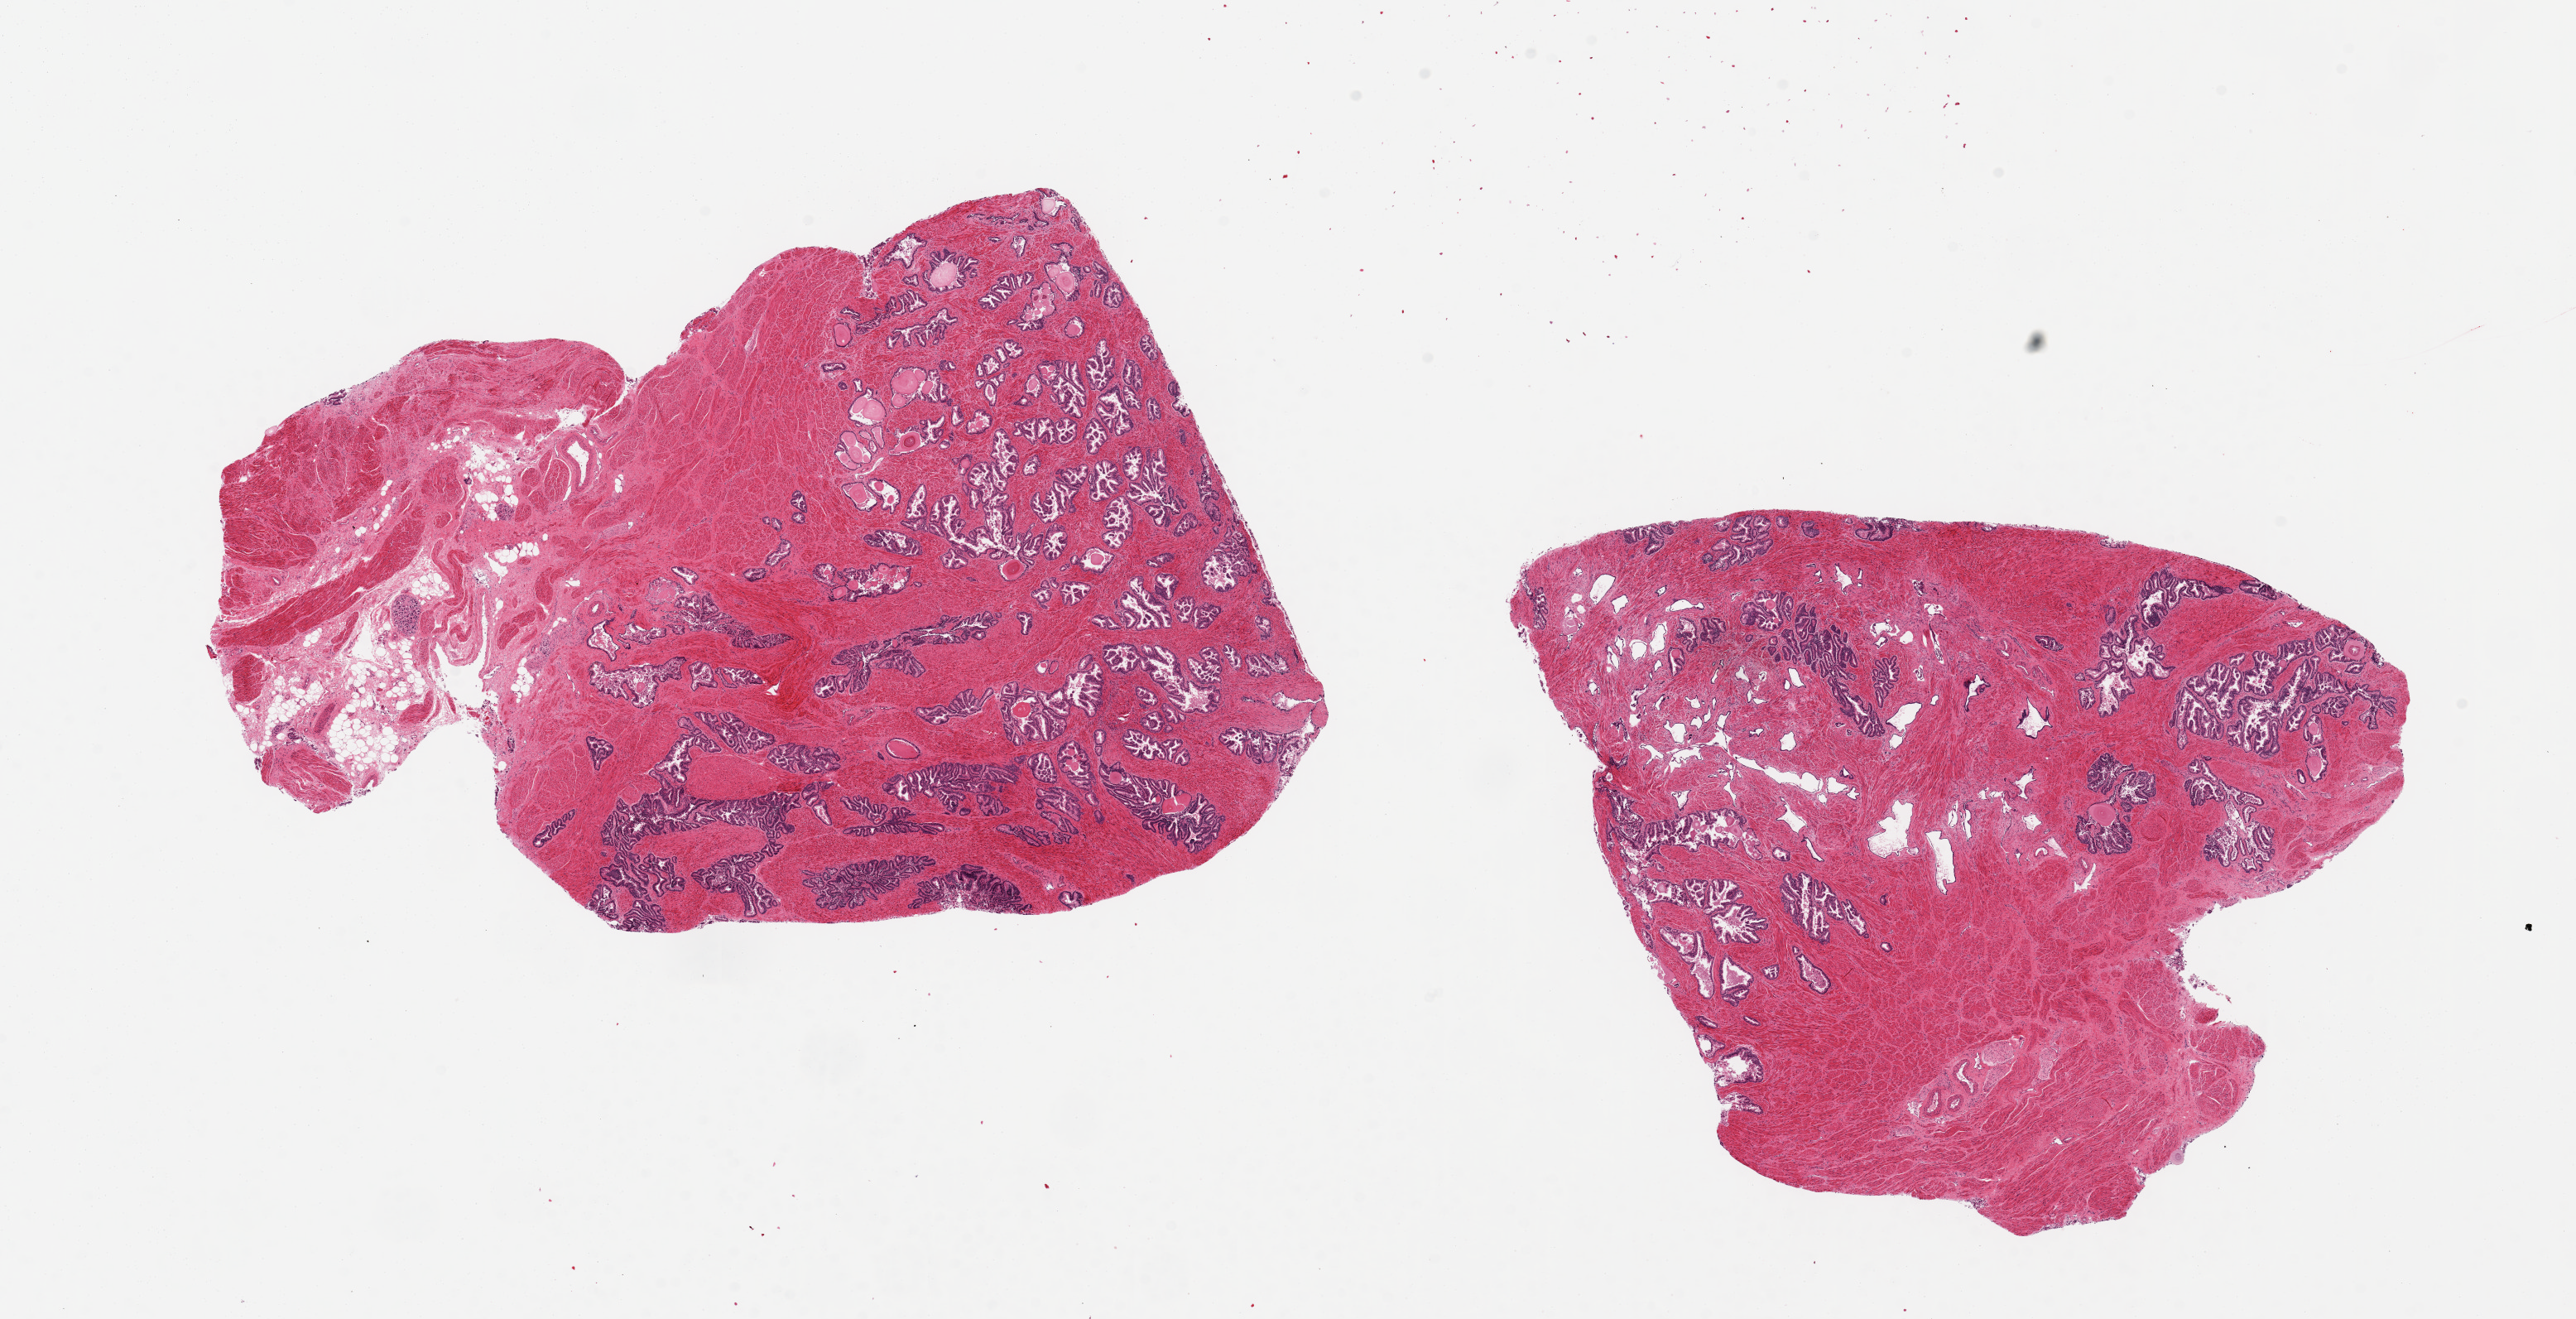
Digitized hematoxylin and eosin (H&E)-stained section — low-resolution overview of the scanned area, about 24.6 x 12.6 mm; PAXgene-fixed paraffin-embedded (PFPE) section; section of prostate (target tissue); tissue donor sample. Donor: male.
* reviewer comment on this tissue sample: 2 pieces, 11x7 & 9x7mm; glands fairly well preserved